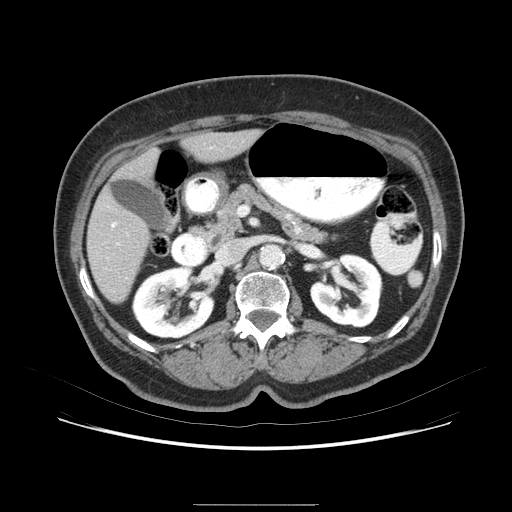
Contrast-enhanced abdominal CT (liver protocol), one axial slice. Position 31 of 79 along the scan axis. 120 kVp. Soft-tissue window (W 400 / L 40 HU). 512 × 512 image matrix, field of view 380 × 380 mm. Case-level facts recorded for this patient, not image findings: diagnosis: hepatocellular carcinoma (patient treated with transarterial chemoembolisation; whether this scan precedes or follows treatment is not stated here); TNM stage (as recorded): Stage-I; Child-Pugh class: A.
Annotated regions visible in this slice (semi-automatic segmentation, software-assisted and operator-edited):
- liver parenchyma outside the tumour (the mass and vessels are separate outlines, so this box may not span the whole liver): bounding box <84,122,270,316> (left, top, right, bottom; pixels)
- mass: <117,201,151,231>
- liver vessels: <123,148,238,295>